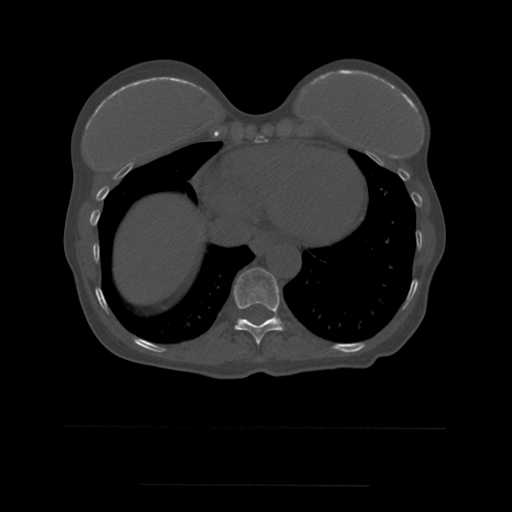
CT including the spine, one axial slice. Slice 300 of 544 in the series (ordered by position). Bone window (W 1800 / L 400 HU). 1.25 mm slice thickness. 512 × 512 image matrix, field of view 350 × 350 mm. Patient age 58 years. Case-level facts recorded for this patient, not image findings: primary cancer: lung.
Outlined on this slice (semi-automatic segmentation, software-assisted and operator-edited):
- T10 vertebra: bounding box [x1, y1, x2, y2] px = [234, 269, 284, 345]
- T11 vertebra: [243, 317, 277, 320]